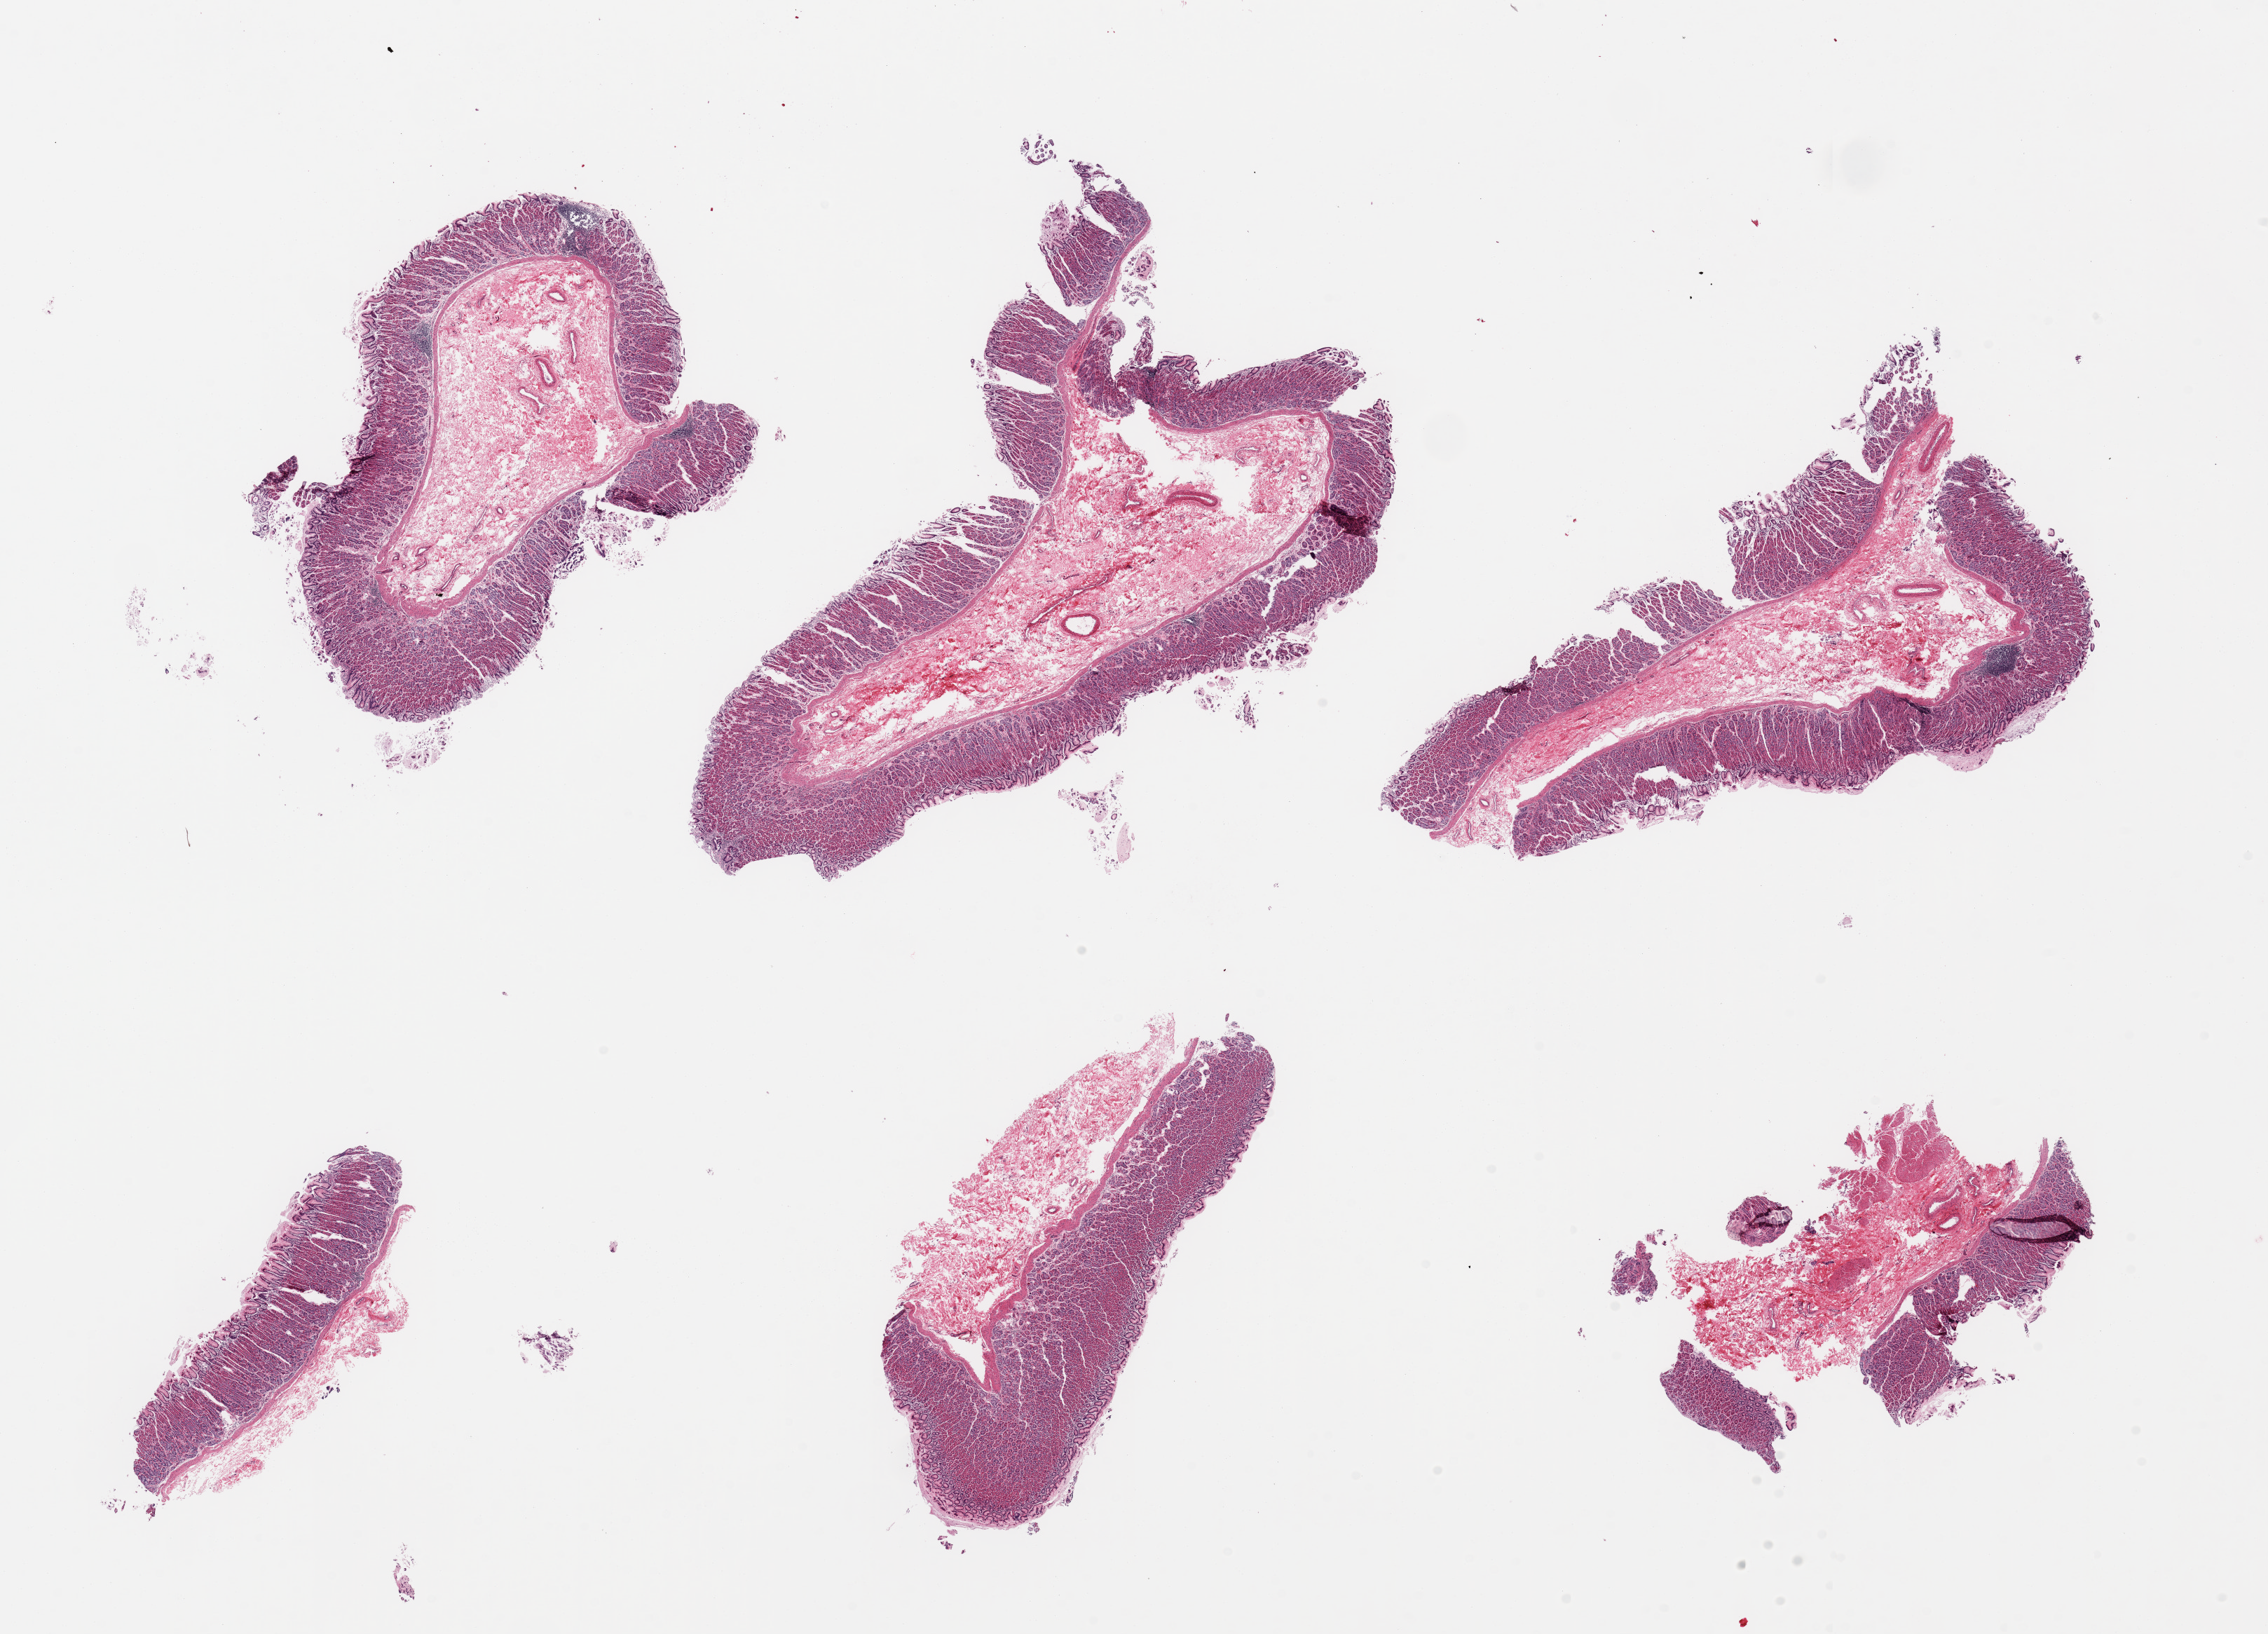
Digitized H&E-stained section — shown as a low-resolution overview of the whole scanned area (about 25.6 x 18.4 mm). Male donor.
* specimen: PAXgene-fixed, paraffin-embedded tissue; section of stomach (target tissue); donor tissue sample